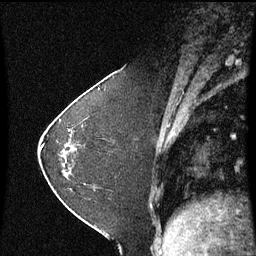
Breast MRI (dynamic contrast-enhanced), one sagittal slice; position 22 of 60 along the scan axis; dynamic contrast-enhanced series, image 2 of 3 at this slice position (ordered by acquisition); 1.5 T; TE 4.2 ms, TR 8.9 ms; 2 mm slice thickness; 256 × 256 image matrix, field of view 200 × 200 mm. Female patient, age 37 years. From the clinical record (not read from this slice): setting: breast cancer imaged before/during neoadjuvant chemotherapy; receptor status: HR-positive, HER2-negative.
Outlined on this slice (semi-automatically segmented with operator editing):
- analysis volume of interest (the breast-tissue region the enhancement analysis was run in; not a lesion): bounding box (x1, y1, x2, y2) in pixels: (60, 102, 122, 181)
- tumour enhancement mask (voxels above the 70 % enhancement threshold inside the analysis volume of interest): (61, 120, 71, 133)